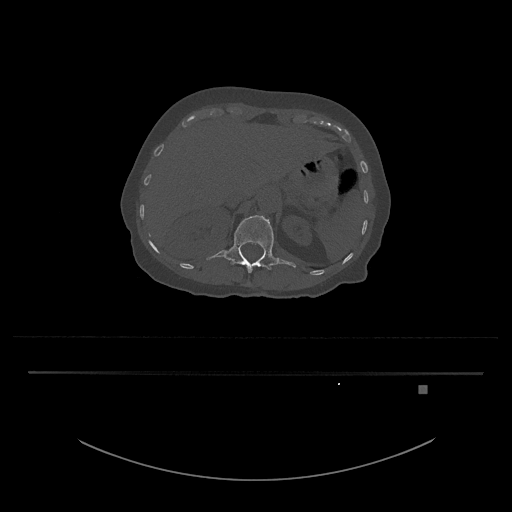
CT including the spine, one axial slice. Position 556 of 797 along the scan axis. Reconstruction kernel Br40s/3. 120 kVp. Bone window (W 1800 / L 400 HU). 0.5 mm slice thickness. 512 × 512 image matrix, field of view 500 × 500 mm. Female patient, age 57 years. Case-level facts recorded for this patient, not image findings: primary cancer: cervical.
Outlined on this slice (semi-automatically segmented with operator editing):
- L1 vertebra: box from (x=207, y=215) to (x=296, y=273) px